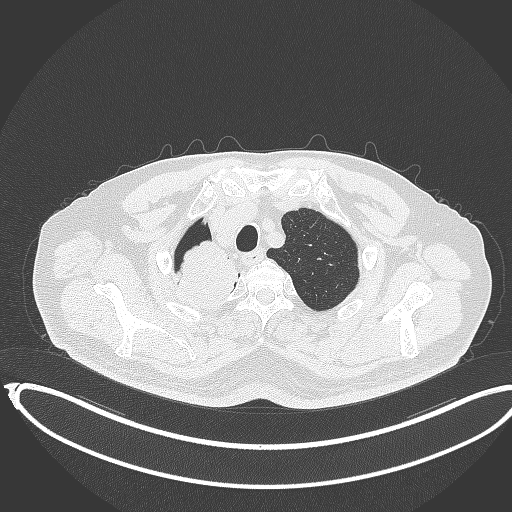
Chest CT, one axial slice; slice 323 of 403 in the series (ordered by position); reconstruction kernel B70f; 120 kVp; lung window (W 1500 / L -600 HU); 512 × 512 image matrix. Male patient, age 68 years. Case-level facts recorded for this patient, not image findings: clinical TNM (as recorded): T2a N0 M0.
Outlined on this slice (rectangle marked by the reading radiologist):
- lung tumour (recorded histology: adenocarcinoma): bounding box <170,240,243,314> (left, top, right, bottom; pixels)